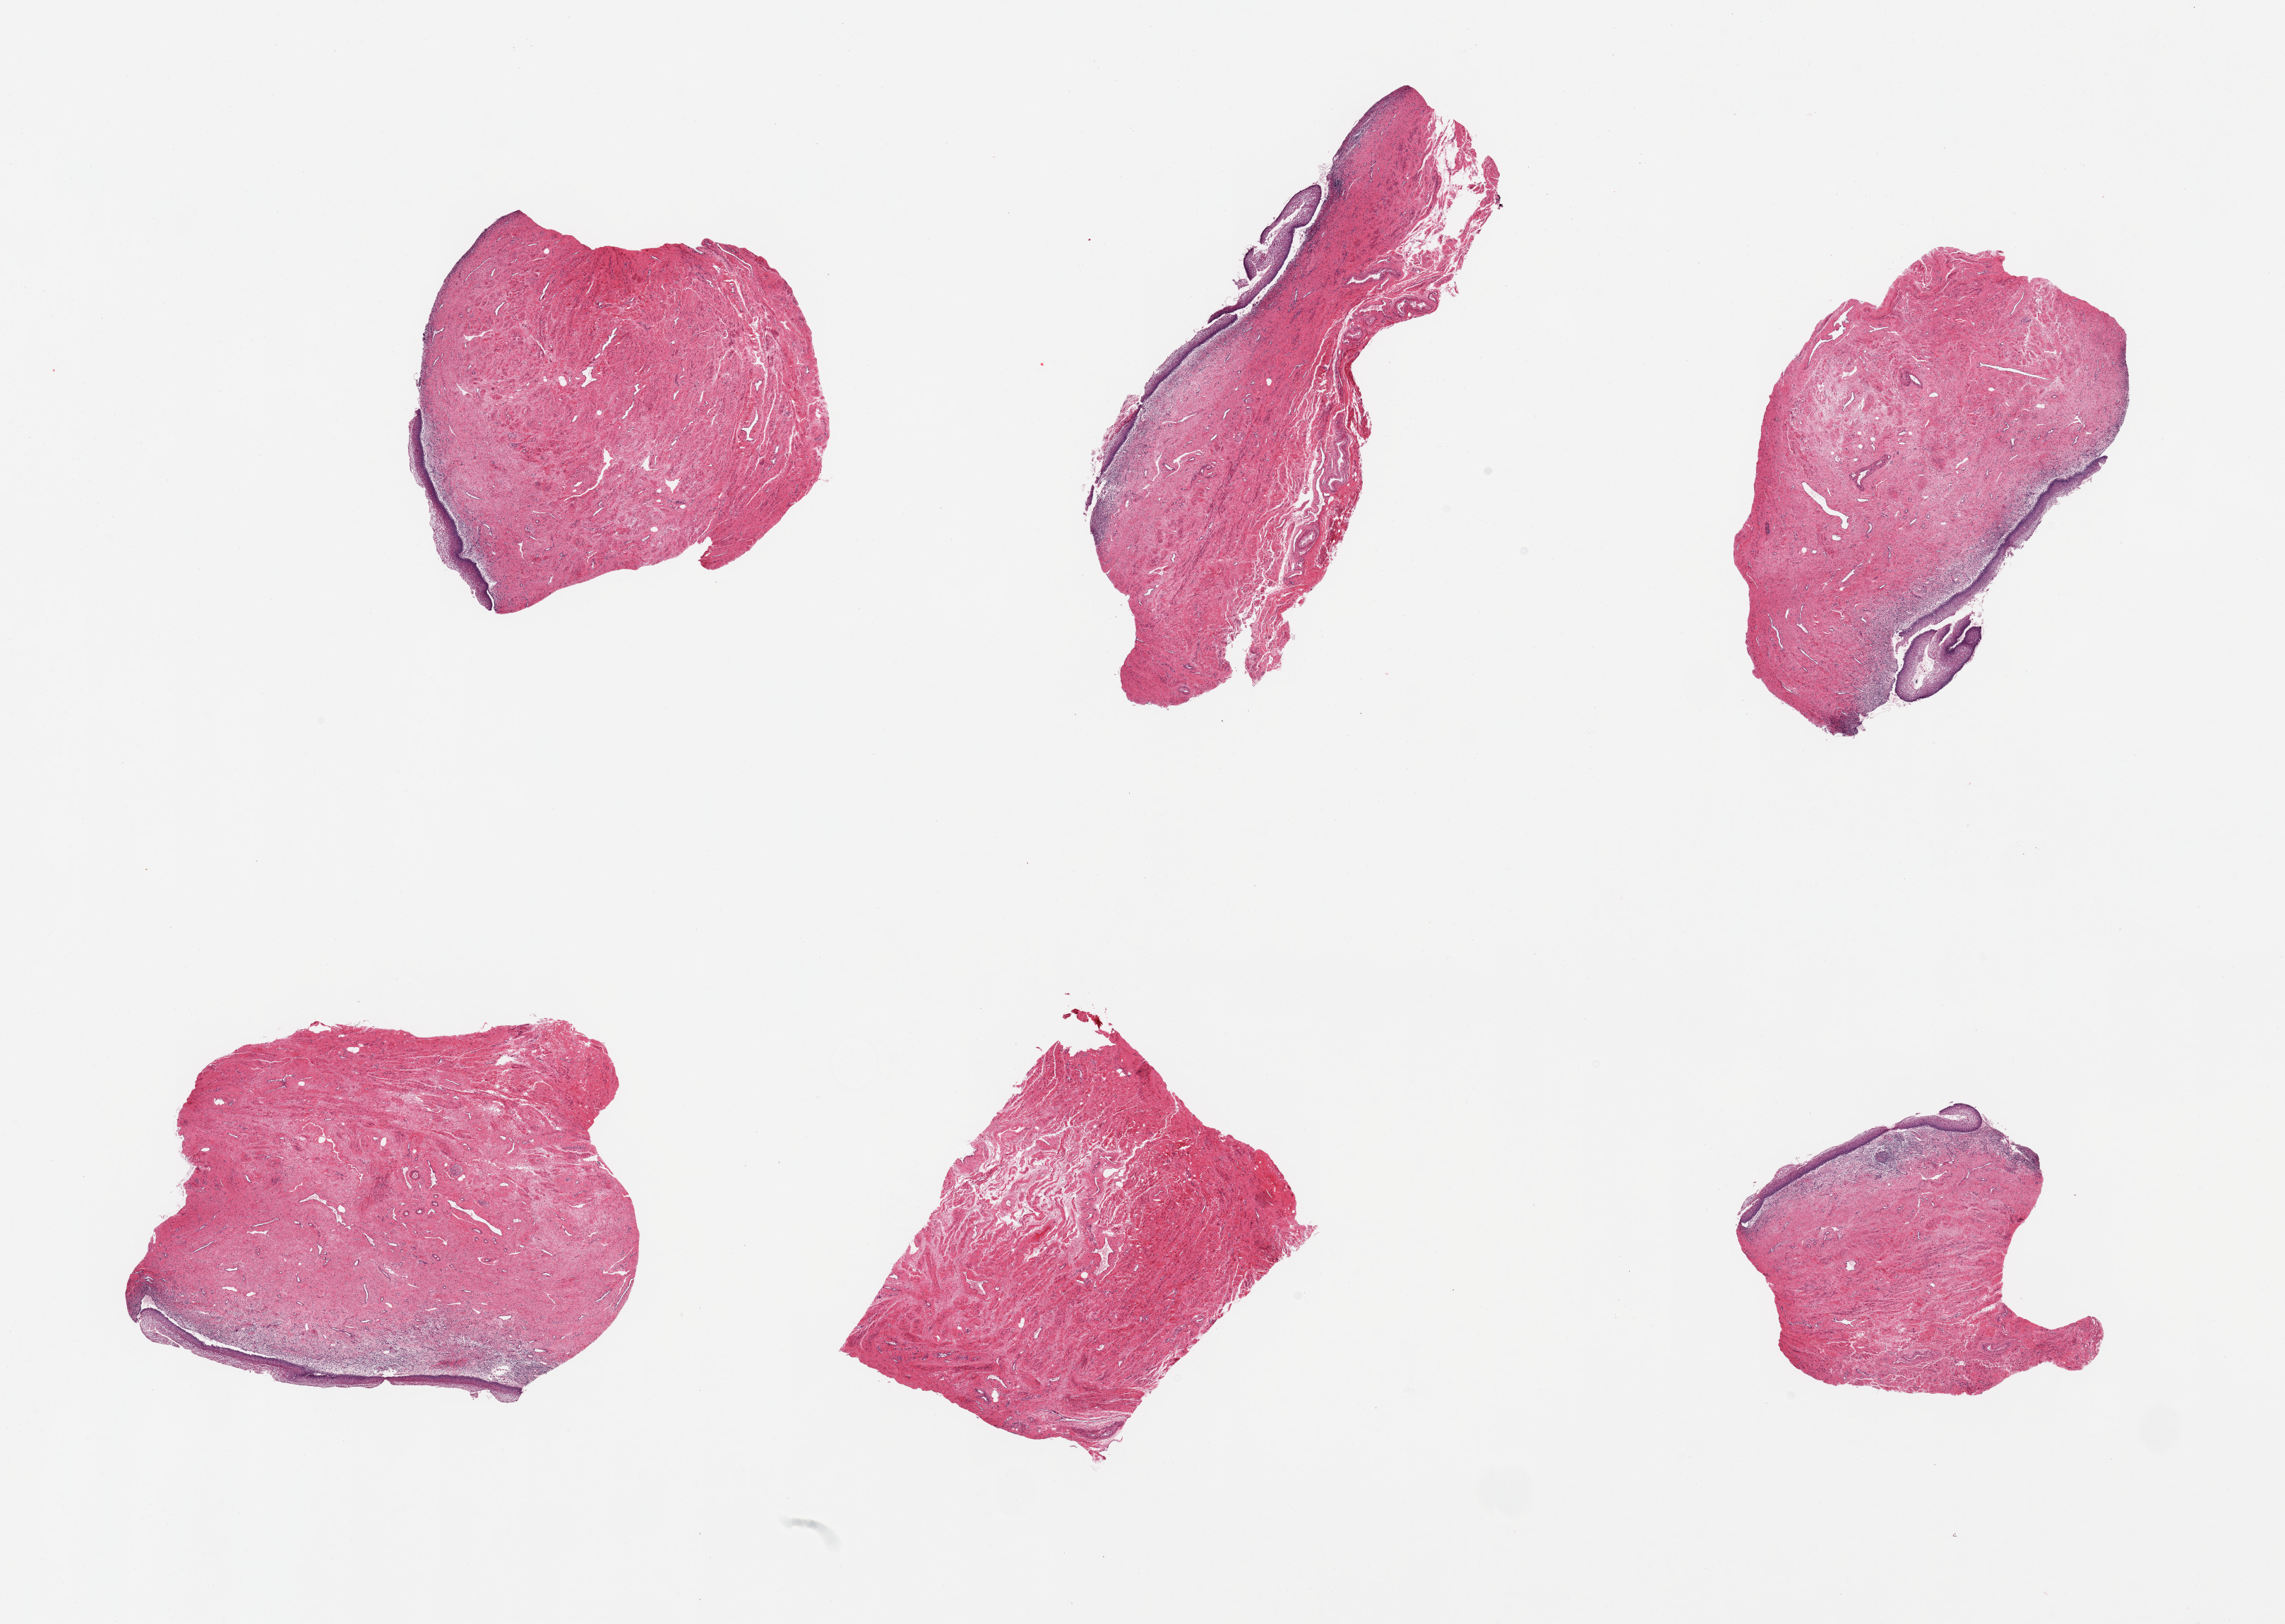
Whole-slide image, hematoxylin and eosin (H&E) stain — low-resolution overview of the scanned area, about 25.6 x 18.2 mm (acquisition: 20x scan). PAXgene-fixed, paraffin-embedded tissue. Target tissue: vagina. Donor tissue sample. Donor sex: female.
Reviewer comment on this tissue sample: 6 pieces, squamous epithelium beginning to slough, patchy chronic vaginitis.